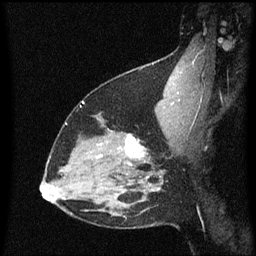
Breast MRI (dynamic contrast-enhanced), one sagittal slice. Position 44 of 60 along the scan axis. Dynamic contrast-enhanced series, image 2 of 3 at this slice position (ordered by acquisition). 1.5 T. TE 4.2 ms, TR 8.4 ms. 2 mm slice thickness. 256 × 256 image matrix, field of view 200 × 200 mm. Patient: female, 38 years. From the clinical record (not read from this slice): setting: breast cancer imaged before/during neoadjuvant chemotherapy; receptor status: HR-positive, HER2-negative.
Annotated regions visible in this slice (semi-automatically segmented with operator editing):
- analysis volume of interest (the breast-tissue region the enhancement analysis was run in; not a lesion): bounding box <122,132,151,163> (left, top, right, bottom; pixels)
- tumour enhancement mask (voxels above the 70 % enhancement threshold inside the analysis volume of interest): <125,134,146,159>